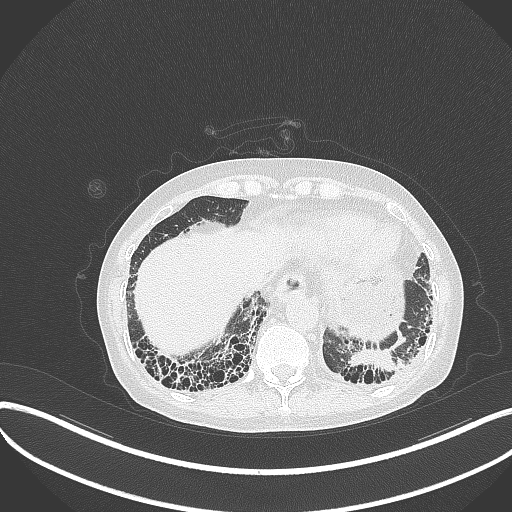
Chest CT, one axial slice. Slice 59 of 373 in the series (ordered by position). Reconstruction kernel B70f. Lung window (W 1500 / L -600 HU). 1 mm slice thickness. 512 × 512 image matrix, field of view 400 × 400 mm. Patient: female, 56 years. From the clinical record (not read from this slice): clinical TNM (as recorded): T1 N0 M0.
Structures marked on this image (rectangle marked by the reading radiologist):
- lung tumour (recorded histology: adenocarcinoma): bounding box [x1, y1, x2, y2] px = [348, 350, 399, 373]